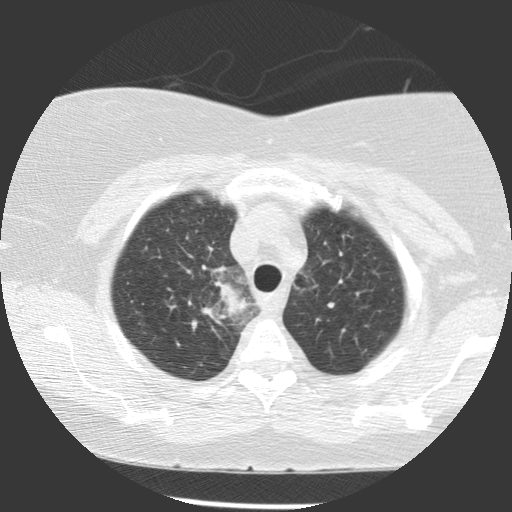
Low-dose screening chest CT, one axial slice. Position 93 of 116 along the scan axis. 140 kVp. Lung window (W 1500 / L -600 HU). 512 × 512 image matrix, field of view 320 × 320 mm.
Outlined on this slice (manually delineated by an expert):
- lesion 1 (tumor, upper lobe of right lung): bounding box [x1, y1, x2, y2] px = [212, 279, 249, 321]